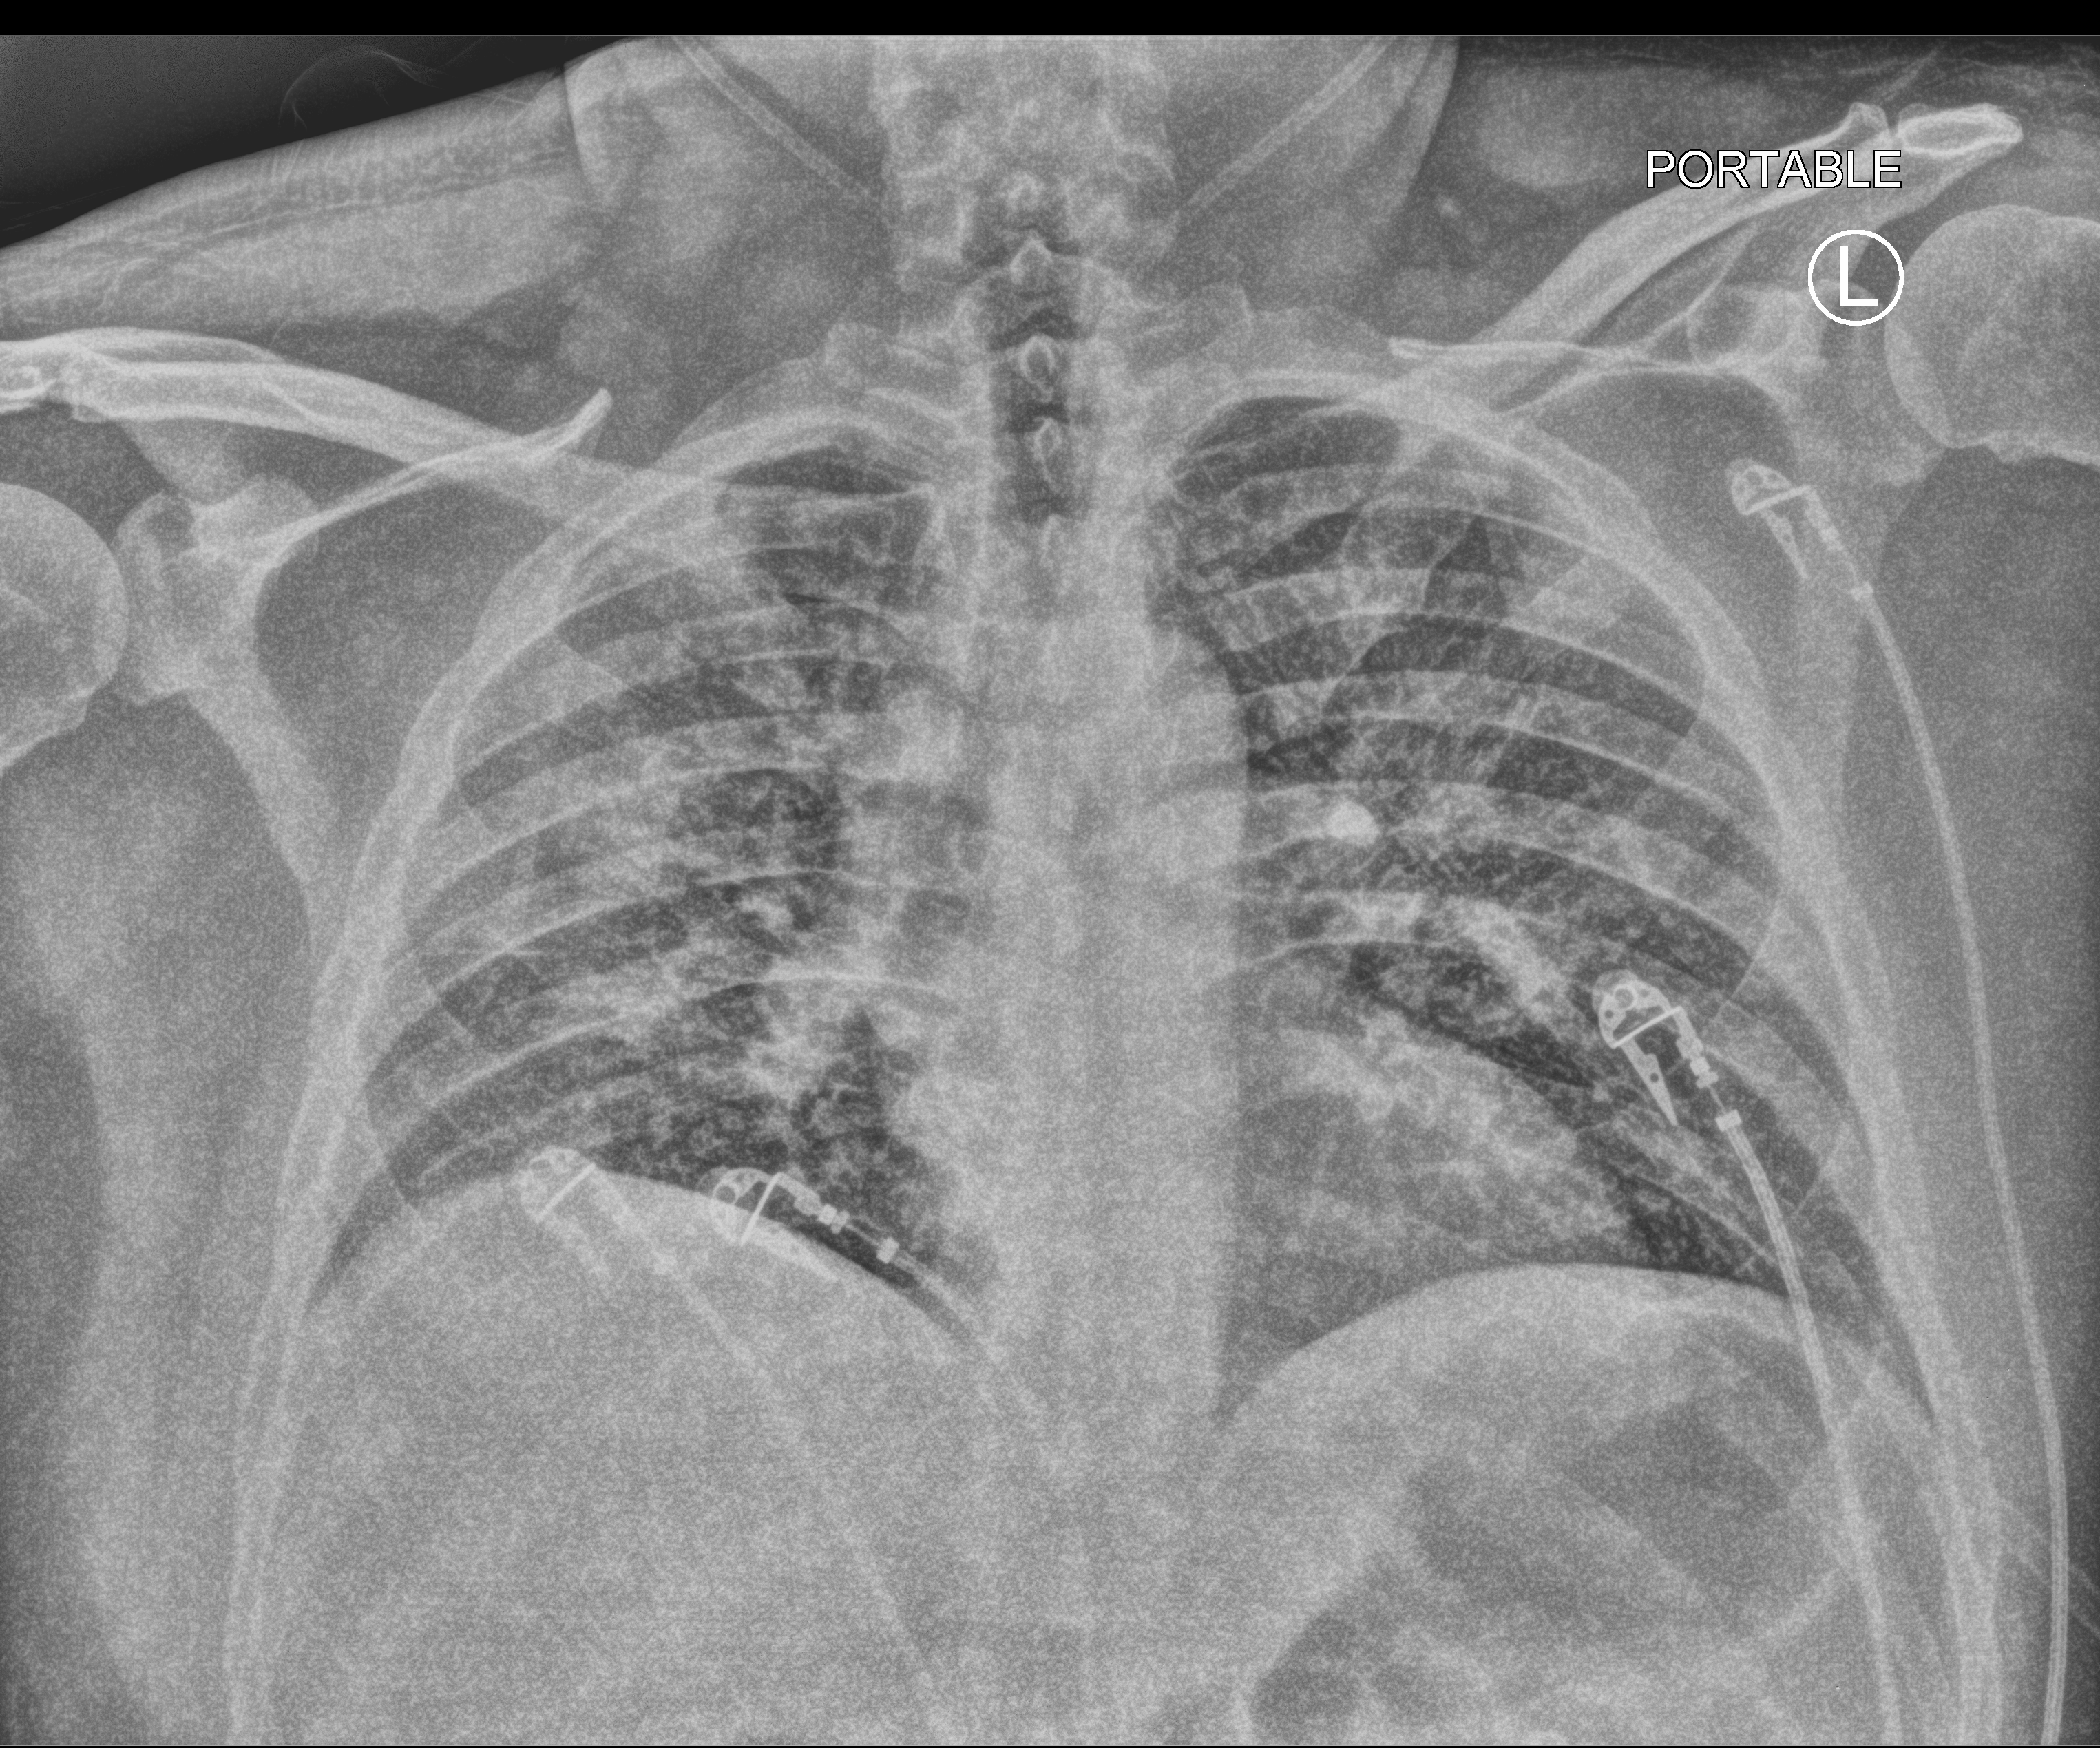
Chest X-ray (portable); anteroposterior (AP) projection. Patient hospitalised with COVID-19; male, aged 18–59 years.
Hospital-stay facts (about this admission, not read from this image; timing relative to this image not recorded):
- admitted to intensive care during this hospital stay: yes
- mechanically ventilated during this hospital stay: yes